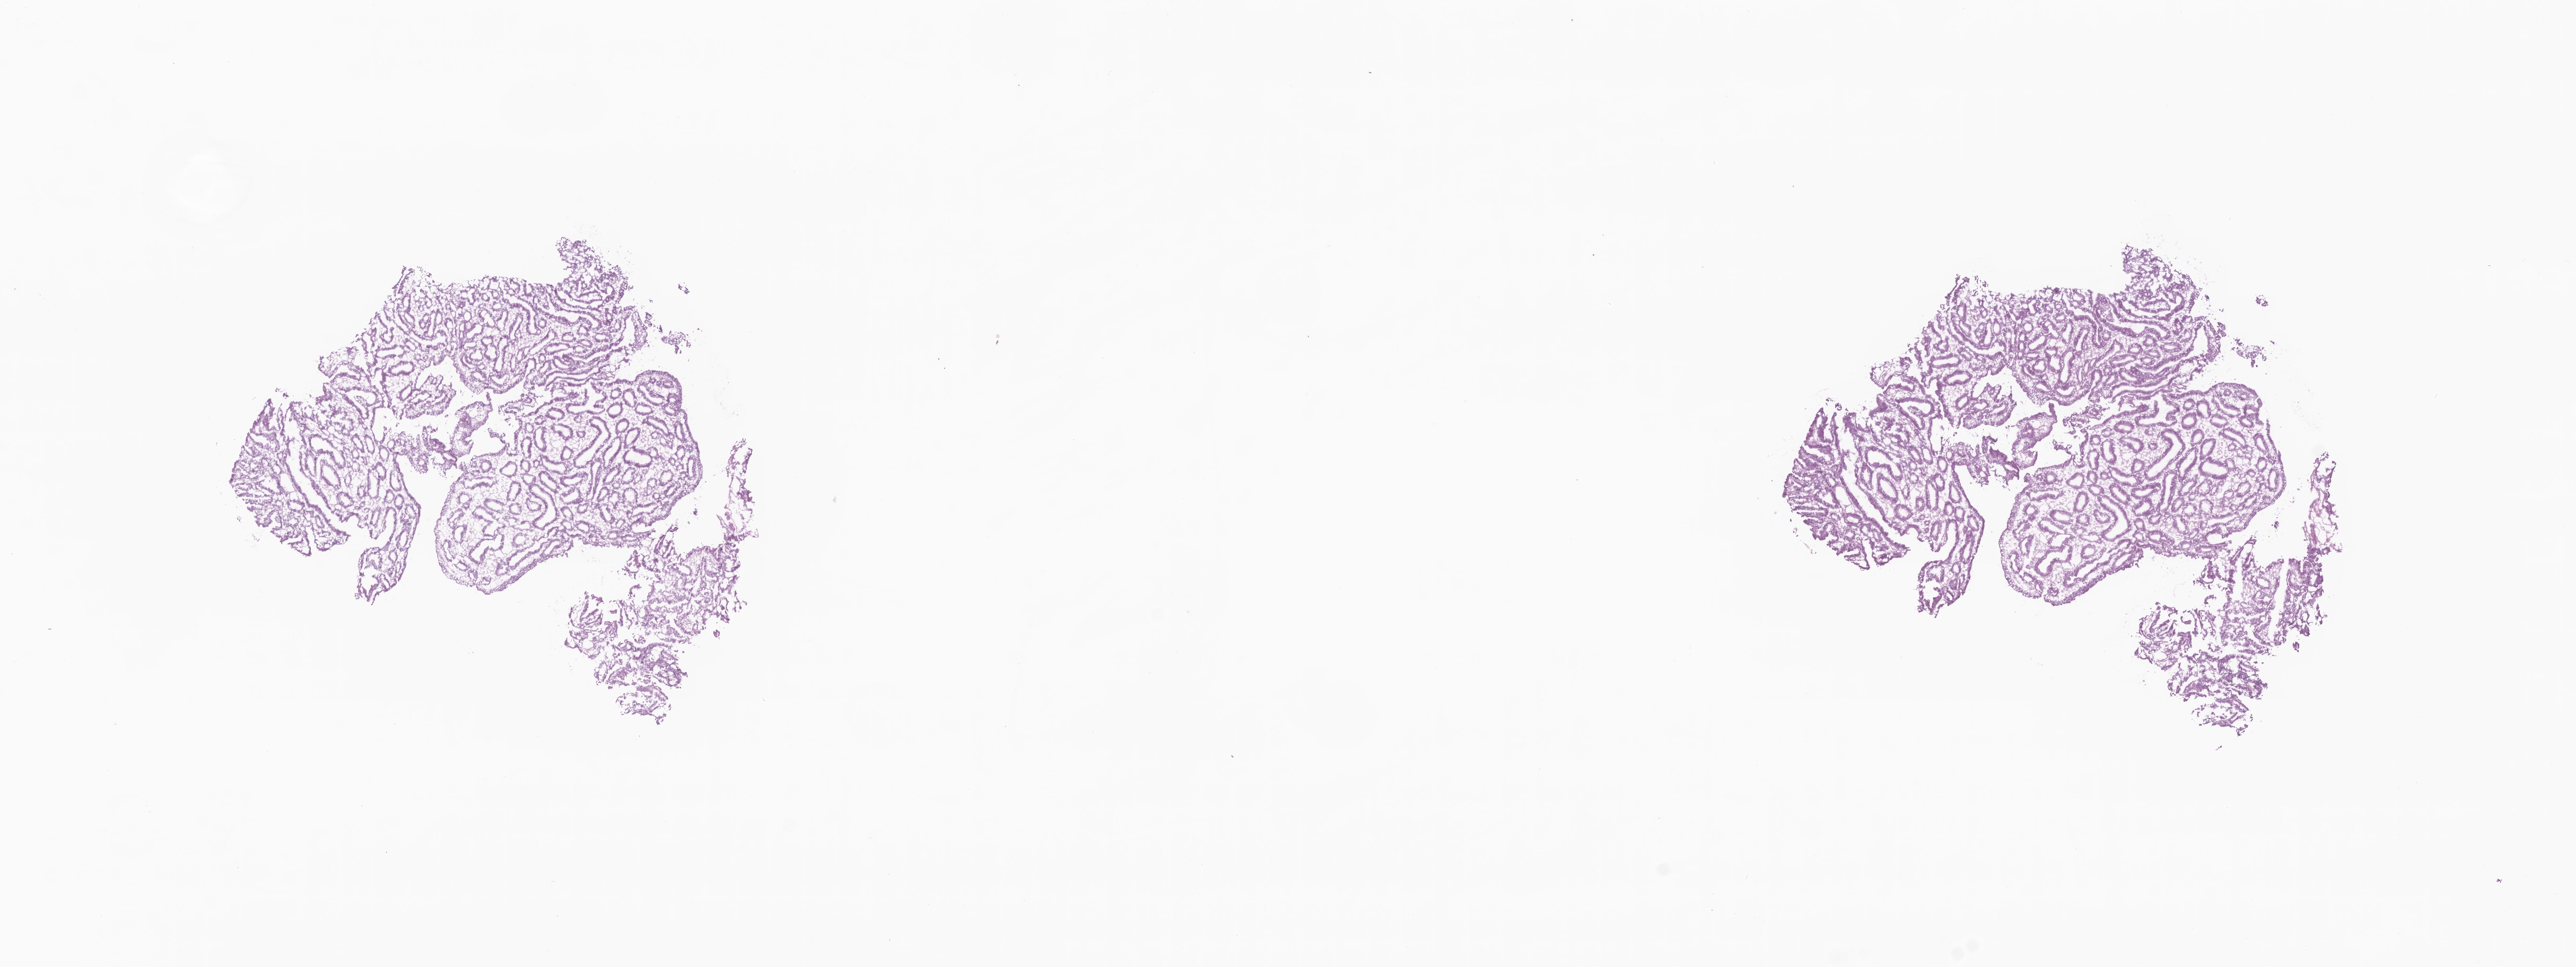
Digitized hematoxylin and eosin (H&E)-stained section, low-resolution overview of the scanned area, about 20.5 x 7.7 mm. Frozen section. Specimen: premalignant lesion from a patient with adenocarcinoma, NOS. Anatomic site: ampulla of vater. Female, age 70 years at initial diagnosis. Composition of this section per pathologist review: tumor cells 0%, tumor nuclei 75%, stromal cells 100%, necrosis 0%, normal cells 0%. Infiltration values recorded for this section: lymphocyte infiltration 5%, monocyte infiltration 2%, neutrophil infiltration 5%.
This section: sample classed premalignant; the patient's recorded diagnosis is given above. Section: top of the tissue portion.